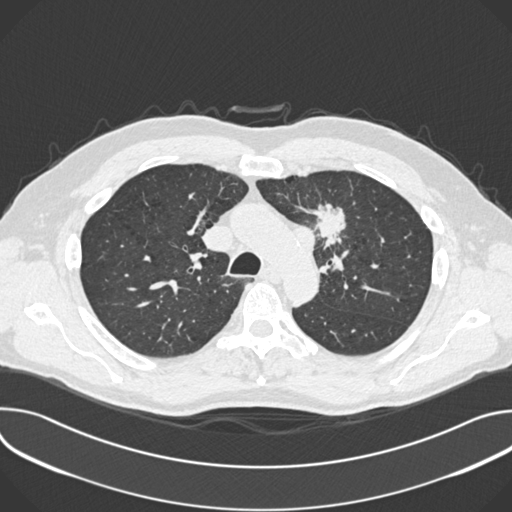
Low-dose screening chest CT, one axial slice. Slice 265 of 361 in the series (ordered by position). Reconstruction kernel B30f. 120 kVp. Lung window (W 1500 / L -600 HU). 512 × 512 image matrix.
Outlined on this slice (outlined manually by an expert reader):
- lesion 1 (tumor, upper lobe of left lung): bounding box [x1, y1, x2, y2] px = [313, 207, 346, 246]